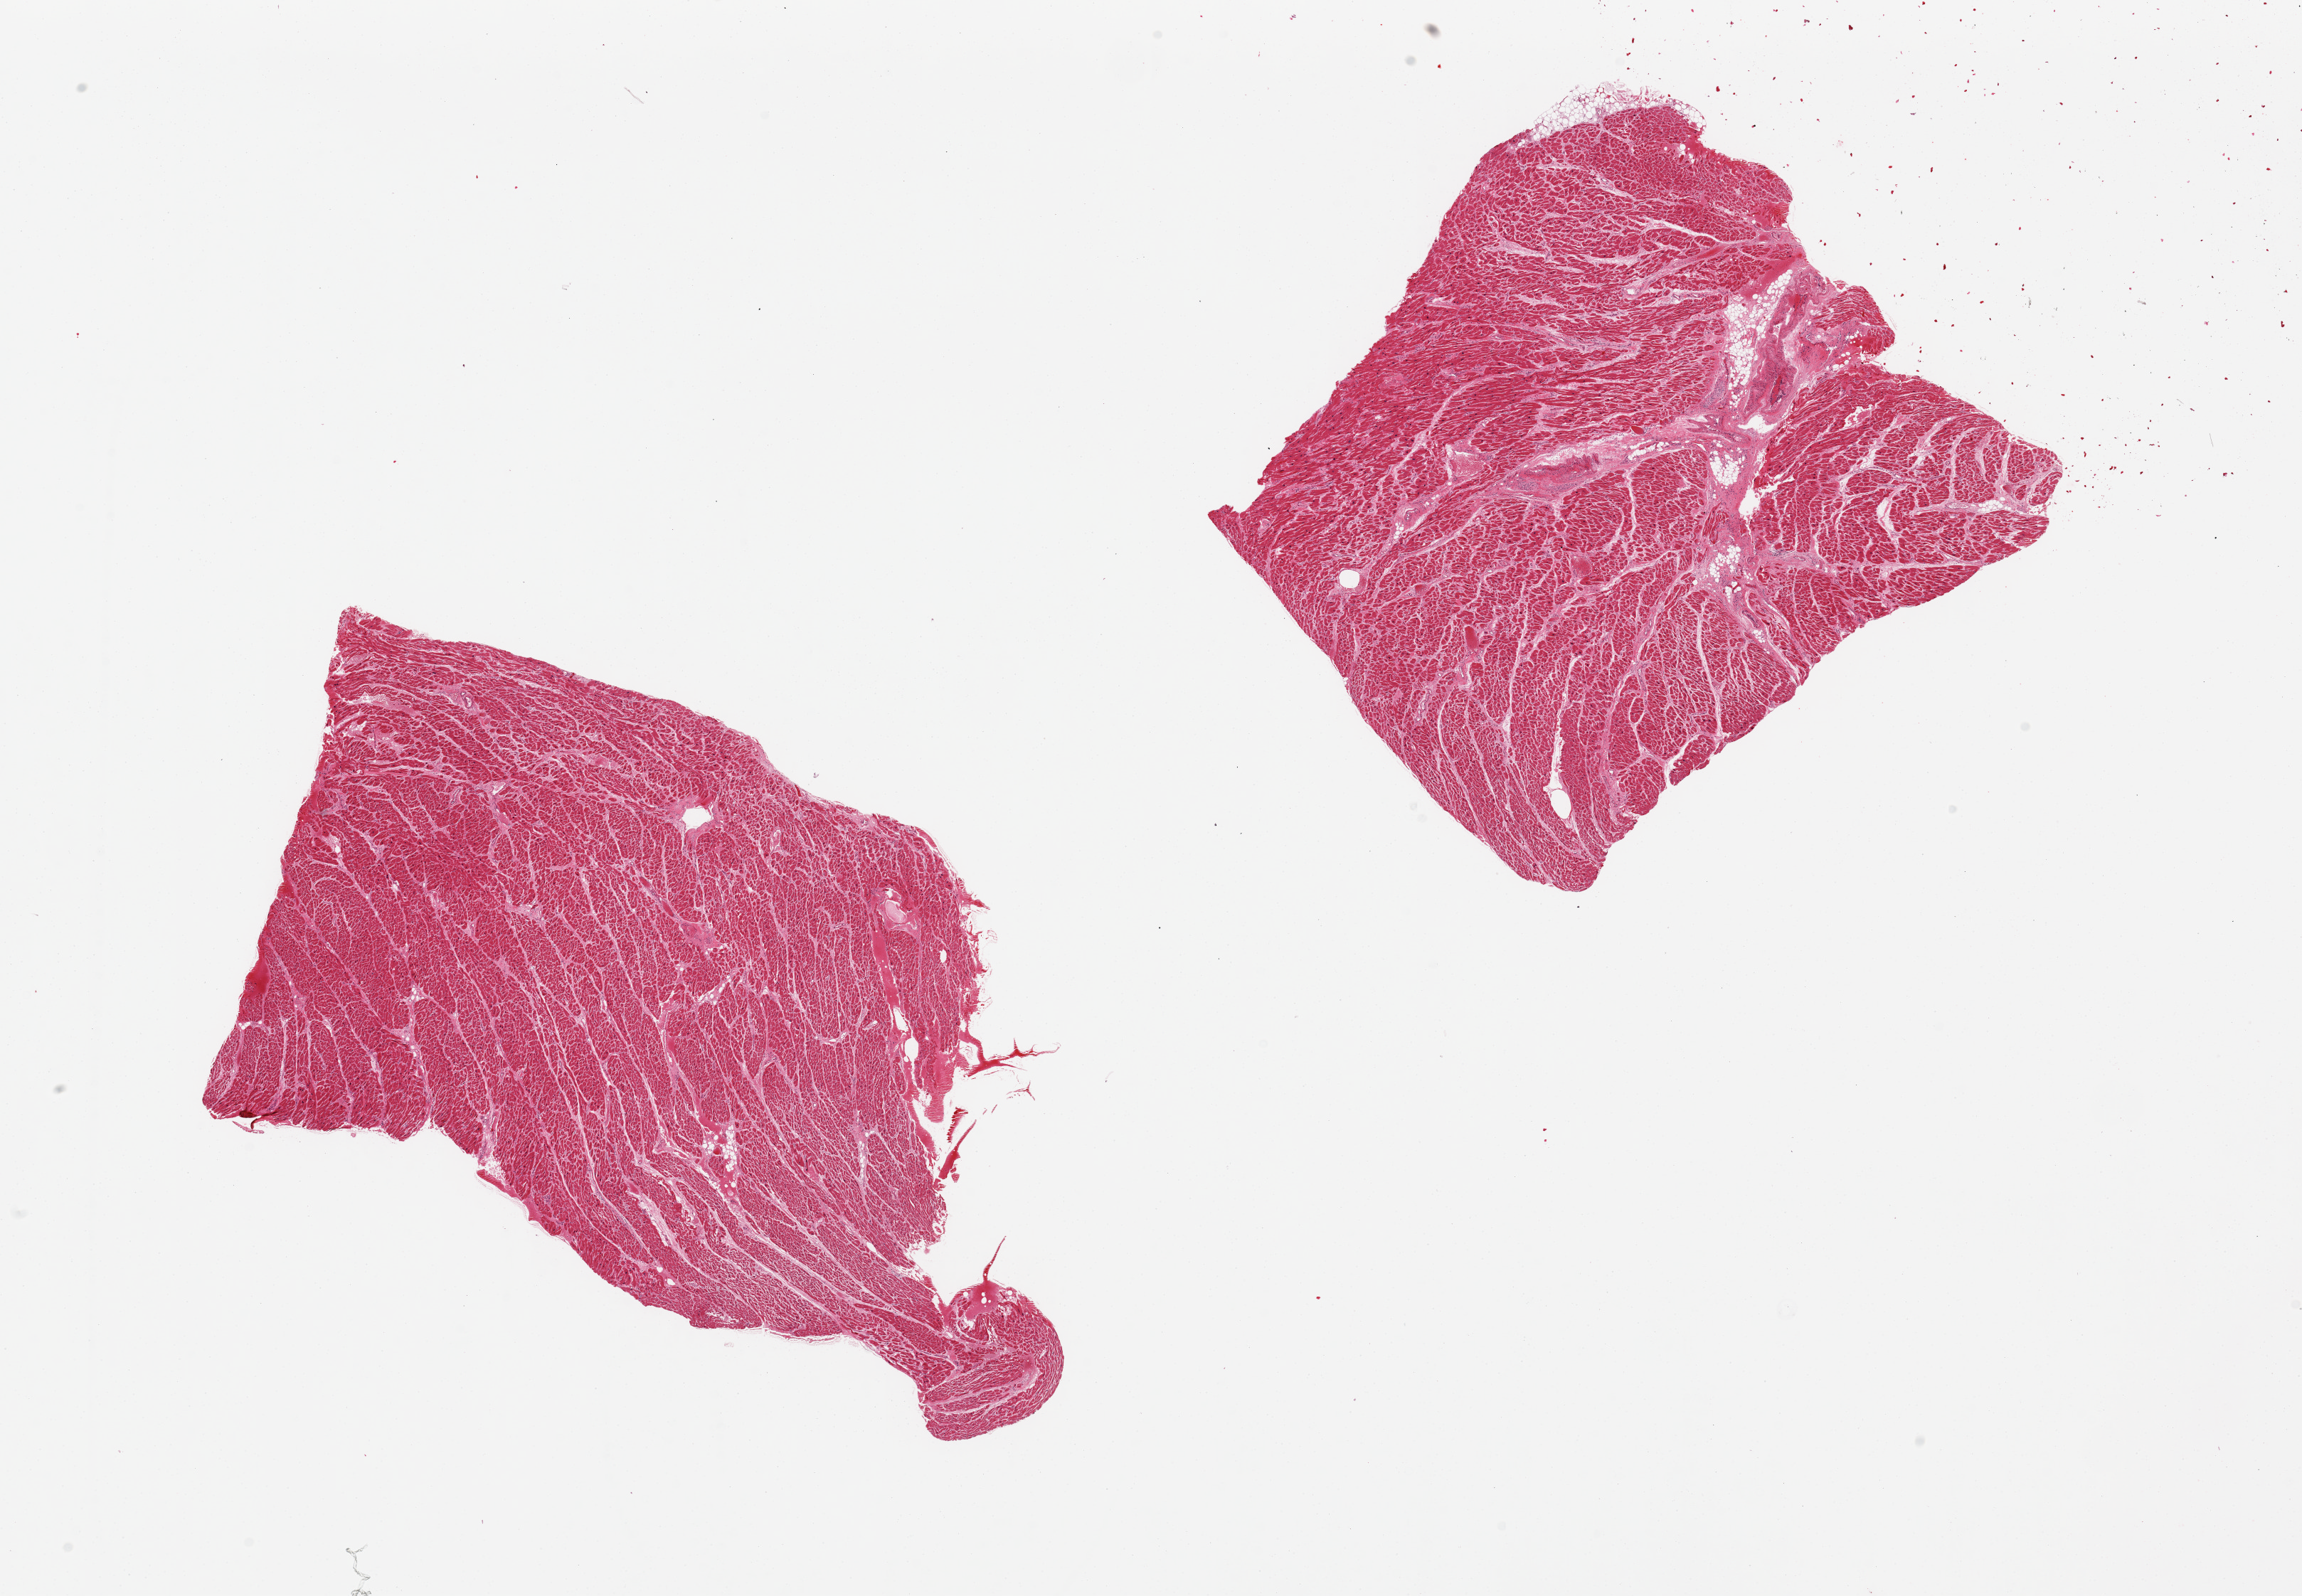
Digitized H&E-stained section, a low-resolution overview of the entire scanned area, about 25.6 x 17.7 mm; PAXgene-fixed paraffin-embedded (PFPE) section; target tissue: heart; tissue donor sample. Donor sex: female.
Pathologist's review note for this sample: 2 pieces, mild-moderate interstitial fibrosis, mild ischemic changes.